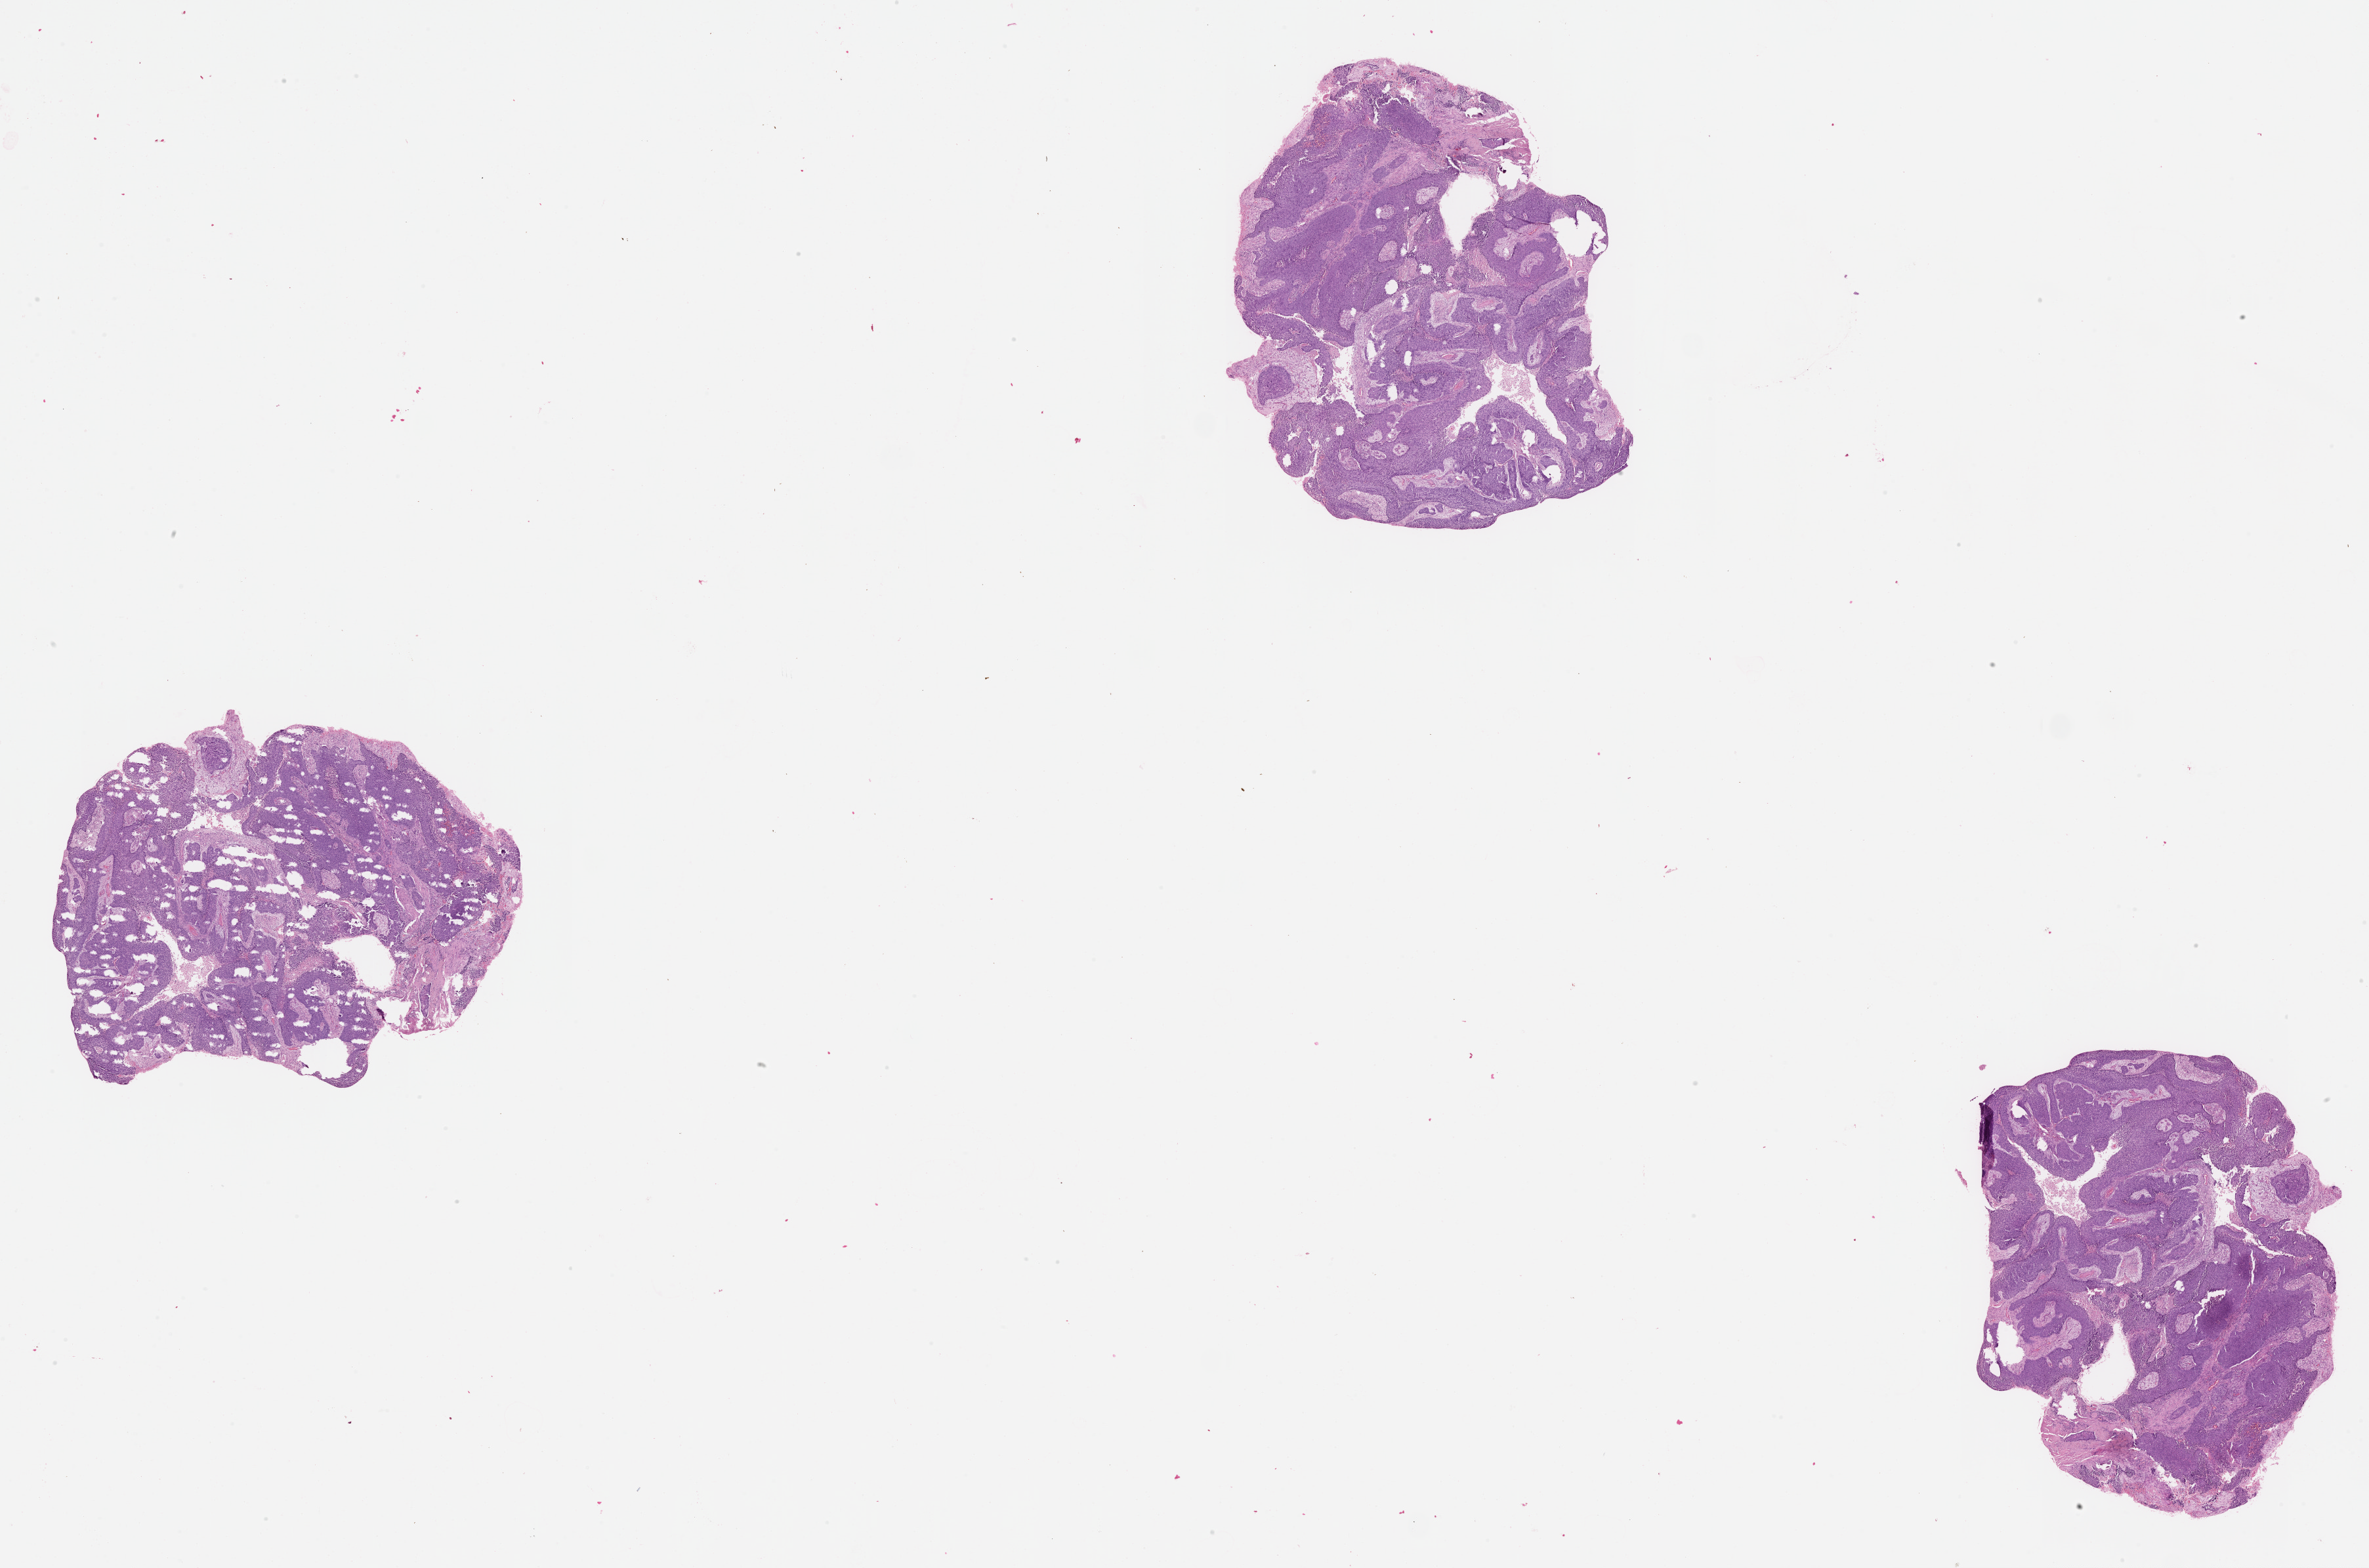
Digitized H&E tissue section (whole slide) — low-resolution overview of the scanned area, about 29.1 x 19.2 mm (from a 20x scan), lung, tumour tissue. Male, 59 y/o.
• patient diagnosis (cohort enrolment): squamous cell carcinoma (lung)